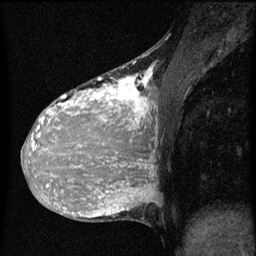
Breast MRI (dynamic contrast-enhanced), one sagittal slice. Position 24 of 60 along the scan axis. Dynamic contrast-enhanced series, image 2 of 3 at this slice position (ordered by acquisition). 1.5 T. TE 4.2 ms, TR 8 ms. 2 mm slice thickness. 256 × 256 image matrix. Patient: female, 36 years.
Annotated regions visible in this slice (semi-automatic segmentation, software-assisted and operator-edited):
- analysis volume of interest (the breast-tissue region the enhancement analysis was run in; not a lesion): box from (x=32, y=68) to (x=161, y=161) px
- tumour enhancement mask (voxels above the 70 % enhancement threshold inside the analysis volume of interest): (x=32, y=68)–(x=153, y=161)